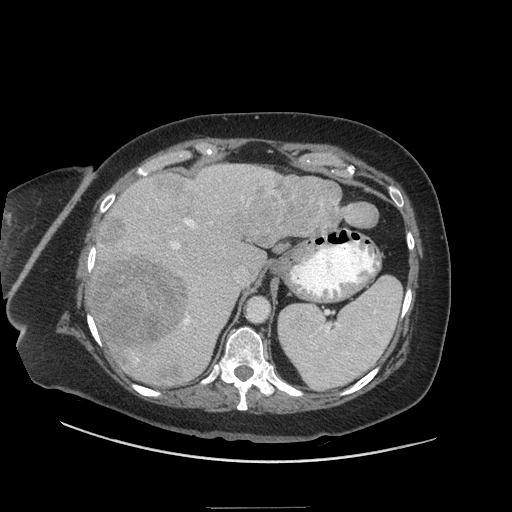
Contrast-enhanced abdominal CT (liver protocol), one axial slice. Slice 40 of 81 in the series (ordered by position). Reconstruction kernel STANDARD. 140 kVp. Soft-tissue window (W 400 / L 40 HU). 2.5 mm slice thickness. 512 × 512 image matrix, field of view 440 × 440 mm. Case-level facts recorded for this patient, not image findings: diagnosis: hepatocellular carcinoma (patient treated with transarterial chemoembolisation; whether this scan precedes or follows treatment is not stated here); TNM stage (as recorded): Stage-II; Child-Pugh class: A; tumour differentiation: moderately differentiated; tumour nodularity: multinodular.
Annotated regions visible in this slice (semi-automatically segmented with operator editing):
- liver parenchyma outside the tumour (the mass and vessels are separate outlines, so this box may not span the whole liver): bounding box (x1, y1, x2, y2) in pixels: (88, 164, 341, 386)
- mass: (91, 171, 379, 387)
- liver vessels: (128, 167, 273, 363)